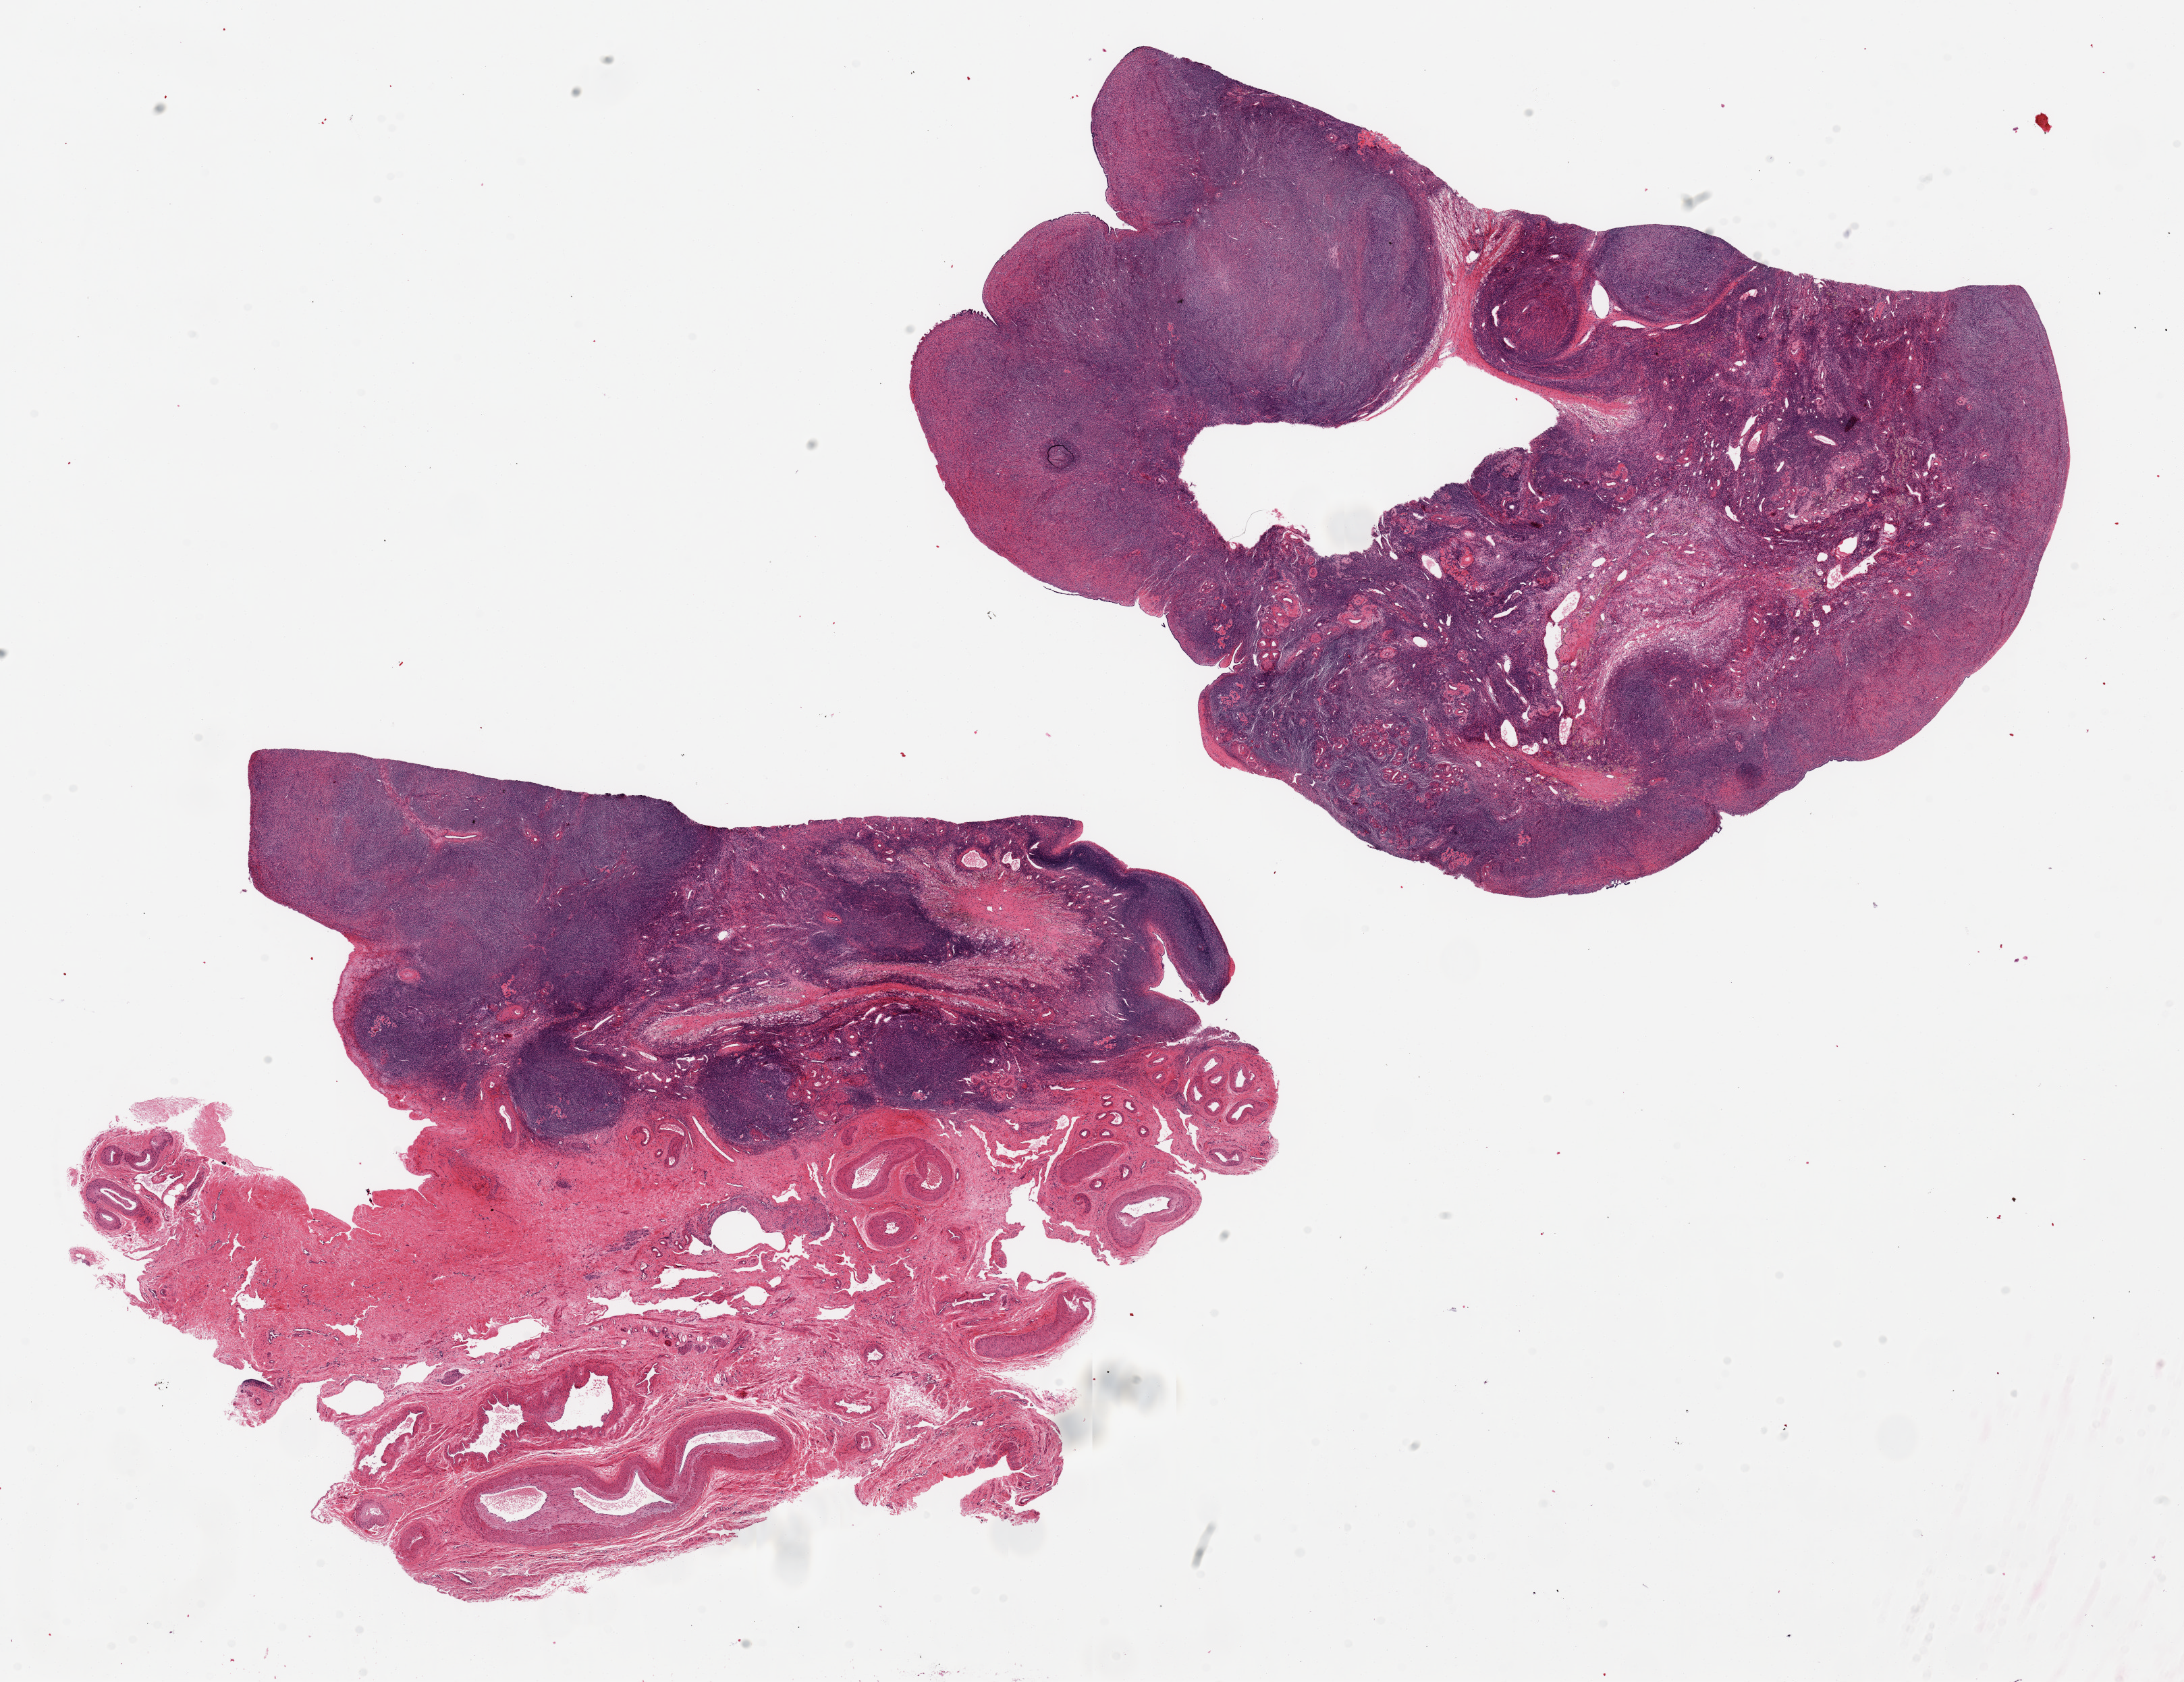
Digitized hematoxylin and eosin (H&E)-stained section, whole scanned area (about 25.6 x 19.7 mm) shown as a low-resolution overview, PAXgene-fixed, paraffin-embedded tissue, target tissue: ovary, tissue donor sample. Donor: female.
Pathologist's review note for this sample: 2 pieces up to 13x8 mm; recent corpora lutea, no ova; 1 with 60% vessels and stroma.